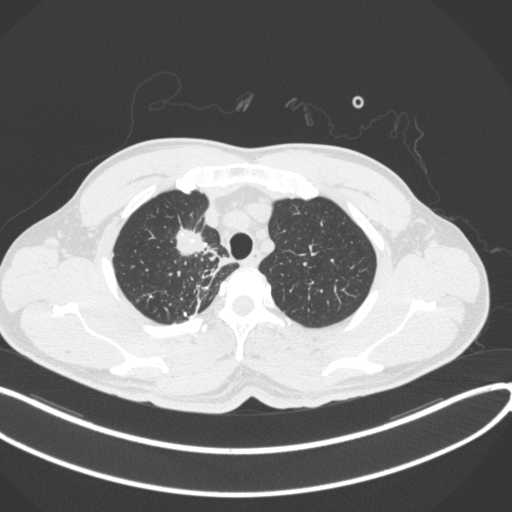
Chest CT, one axial slice; slice 314 of 391 in the series (ordered by position); reconstruction kernel B31f; 120 kVp; lung window (W 1500 / L -600 HU); 512 × 512 image matrix, field of view 400 × 400 mm. Patient: male, 48 years. From the clinical record (not read from this slice): clinical TNM (as recorded): T1c N1 M1.
Annotated regions visible in this slice (bounding box drawn by a radiologist):
- lung tumour (recorded histology: adenocarcinoma): box from (x=169, y=223) to (x=212, y=261) px